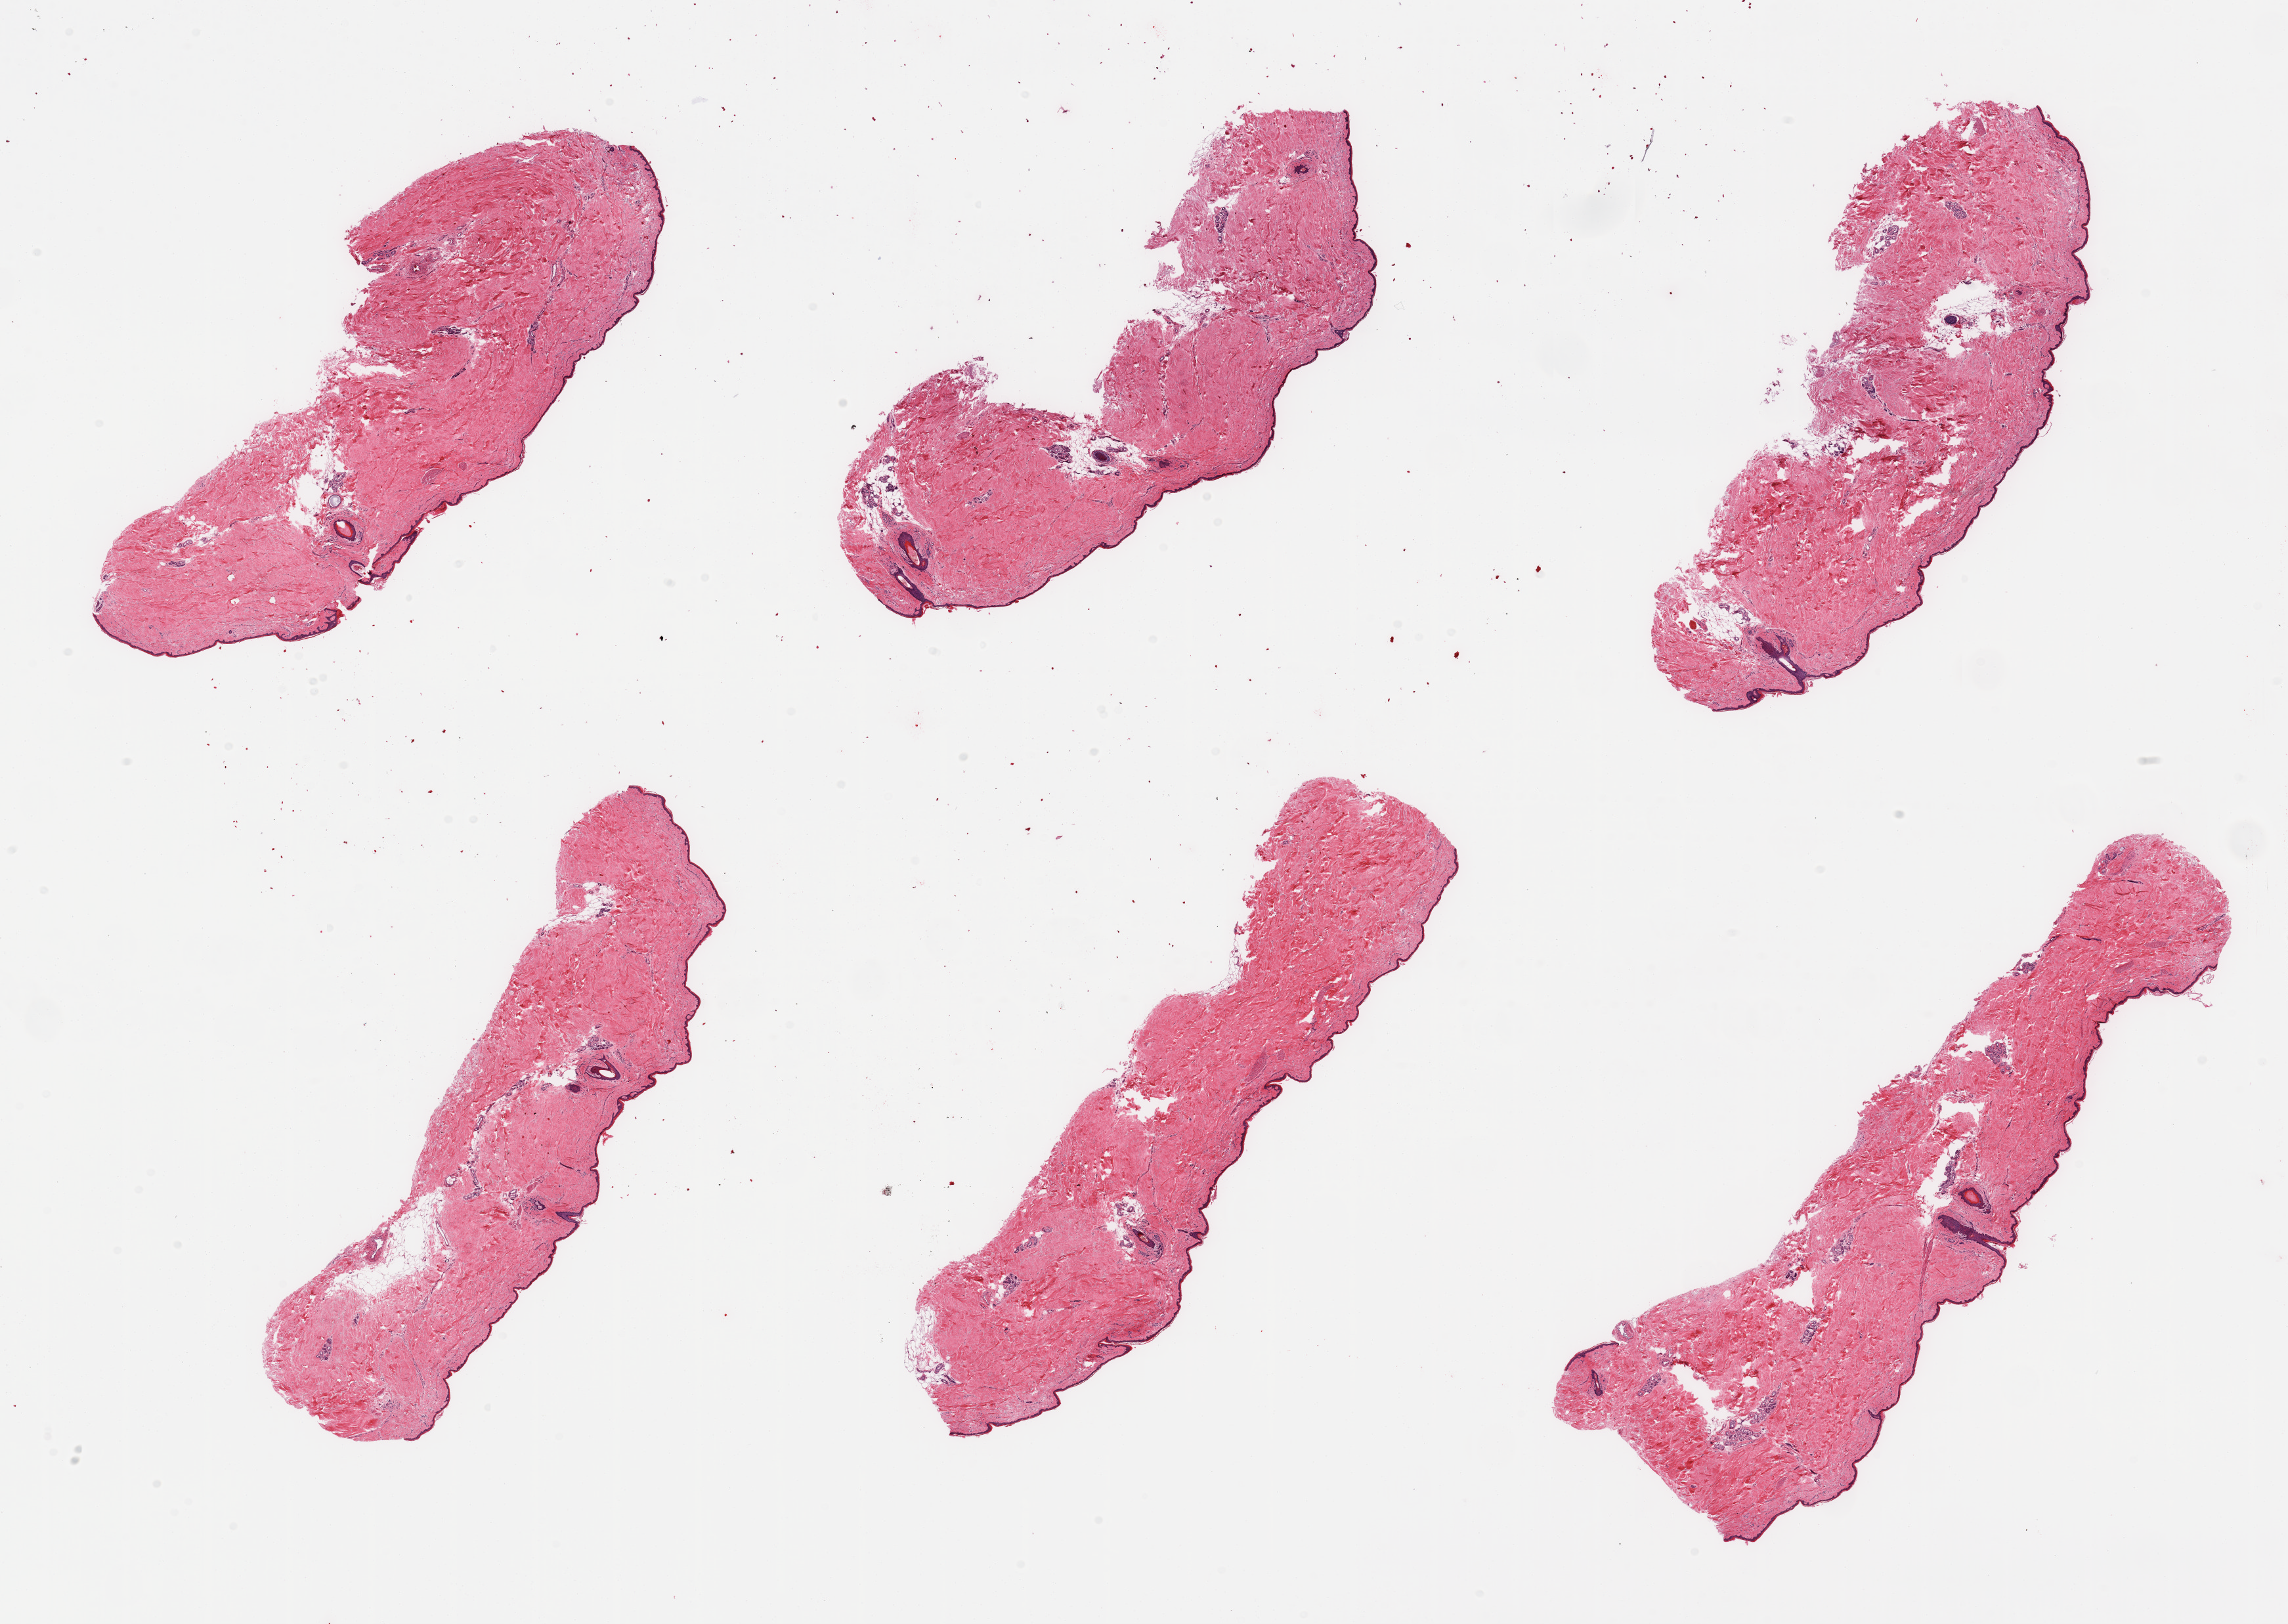
H&E whole-slide image, brightfield, a low-resolution overview of the entire scanned area, about 27.6 x 19.6 mm, PAXgene-fixed paraffin-embedded (PFPE) section, target tissue: skin of lower leg, donor tissue sample. Donor sex: male.
Pathologist's review note for this sample: 6 pieces; well trimmed; 10% dermal fat.